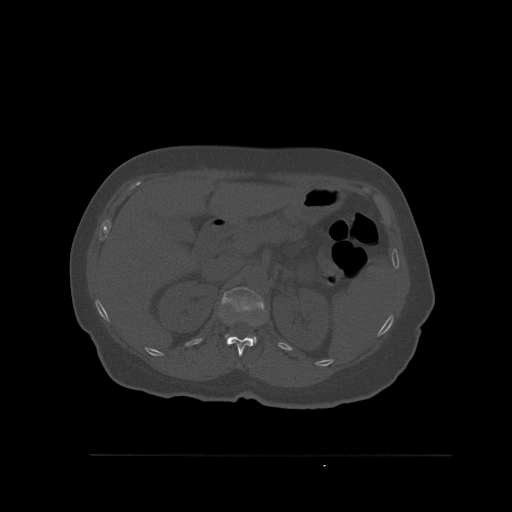
CT including the spine, one axial slice. Position 279 of 527 along the scan axis. Bone window (W 1800 / L 400 HU). 1.5 mm slice thickness. 512 × 512 image matrix, field of view 470 × 470 mm. Female patient, age 73 years. From the clinical record (not read from this slice): primary cancer: breast; vertebrae with lytic lesions (as recorded): L2.
Structures marked on this image (semi-automatically segmented with operator editing):
- L1 vertebra: bounding box <220,287,265,345> (left, top, right, bottom; pixels)
- T12 vertebra: <227,321,257,356>